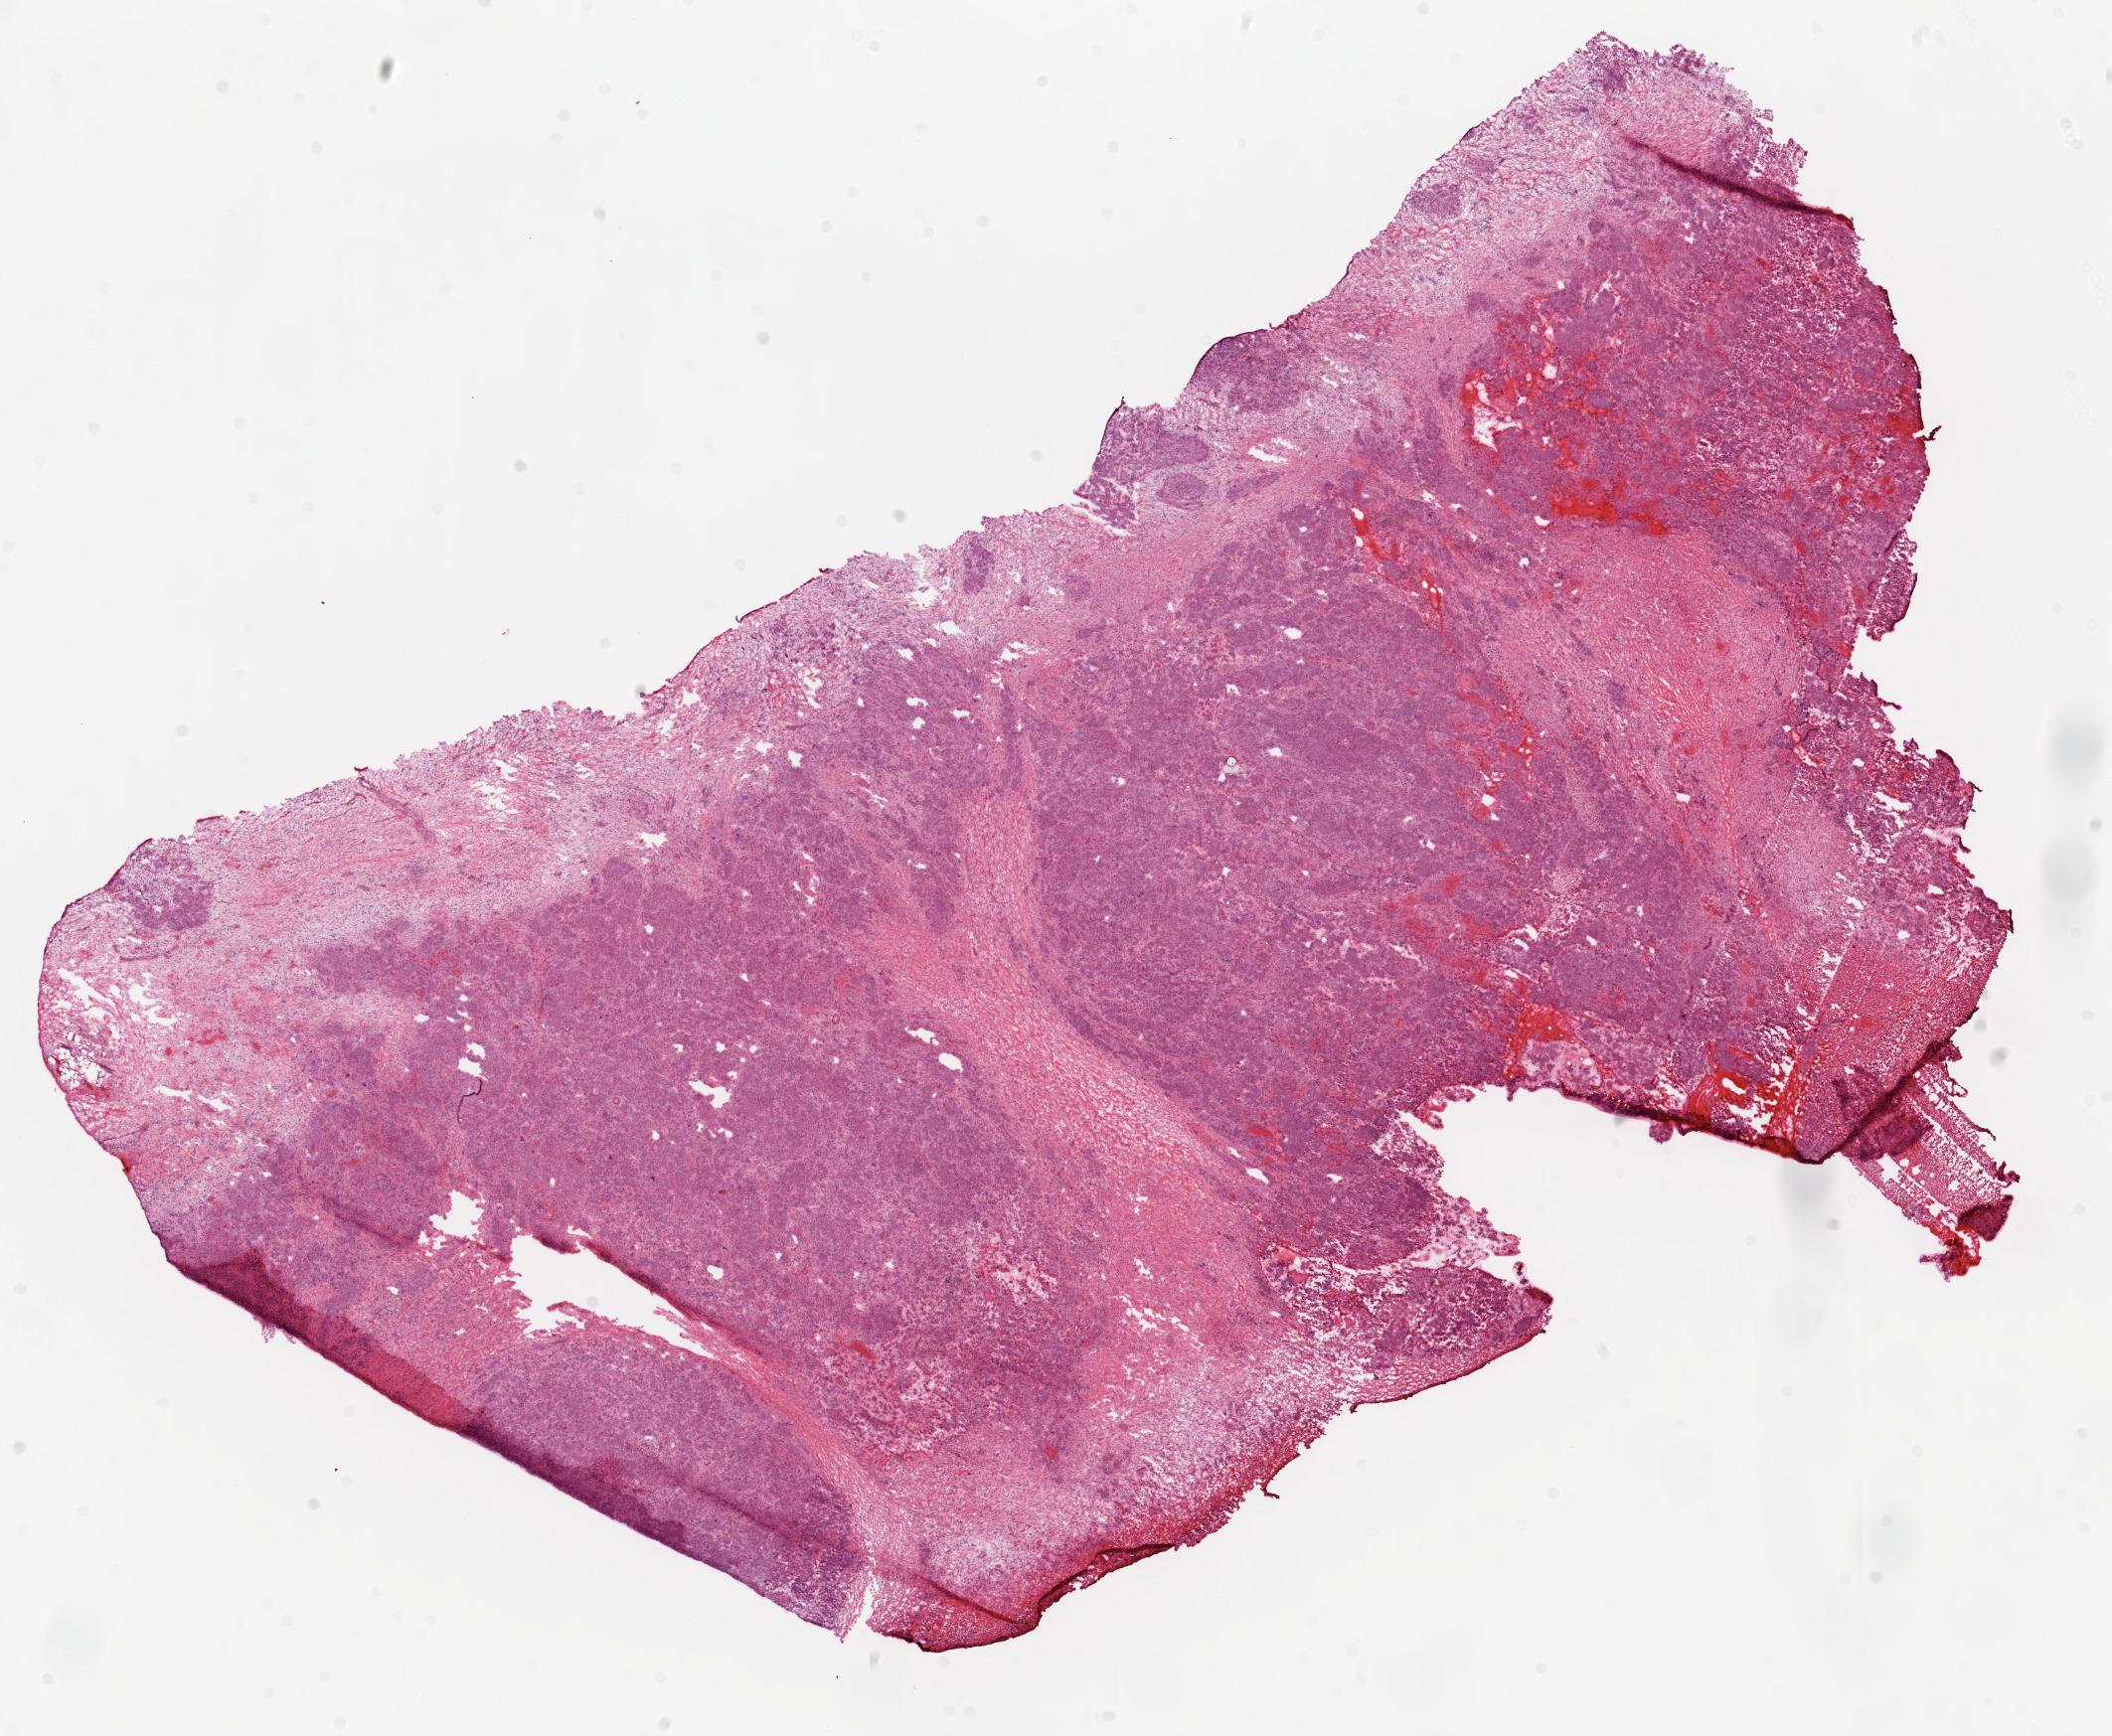
Digitized H&E-stained tissue section (whole slide), whole scanned area (about 17.1 x 14.0 mm, from a 20x scan) shown as a low-resolution overview. Frozen section. Sample: primary tumour, ovary. Female patient; age at initial diagnosis 64 years. Histologic grade: G3 (poorly differentiated). Composition of this section per pathologist review: tumour cells 89%, tumour nuclei 90%, normal cells 0%, stromal cells 10%, necrosis 1%.
FIGO stage: IIIC. Diagnosis: Serous cystadenocarcinoma, NOS.